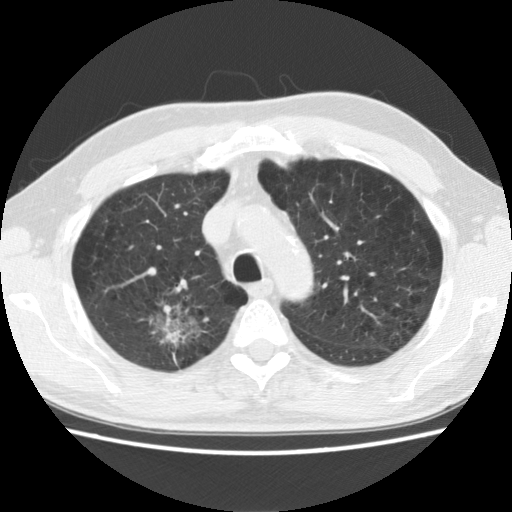
Chest CT (low-dose screening protocol), one axial image, baseline annual screen, lung window (W 1500 / L -600 HU), 2.5 mm slice thickness, standard (soft-tissue) reconstruction kernel (STANDARD), slice 39 of 142 in the series. Male, age 64 years at enrolment. Former smoker at enrolment.
Expert reader's lesion annotation, bounding box [x1, y1, x2, y2] px = [117, 296, 207, 367]. The exam's reader record, not a measurement of the box and not confirmed to be the same lesion: non-calcified nodule or mass ≥4 mm, right upper lobe, 39 × 31 mm, spiculated (stellate) margins, mixed attenuation. Official screen result: positive, change unspecified: nodule(s) >= 4 mm or enlarging nodule(s), mass(es), or other non-specific abnormalities suspicious for lung cancer. Later outcome: lung cancer diagnosed 74 days after this screen — adenocarcinoma, NOS, right upper lobe, moderately differentiated (G2), stage IB (AJCC 6th edition), 40 mm at pathology.